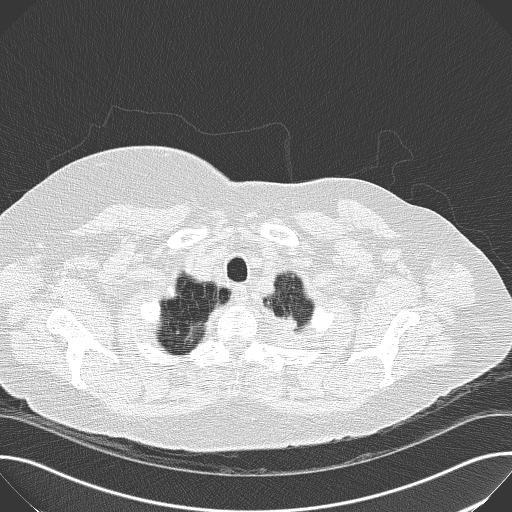
Low-dose screening chest CT, one axial slice; position 155 of 169 along the scan axis; reconstruction kernel B50f; 120 kVp; lung window (W 1500 / L -600 HU); 2 mm slice thickness; 512 × 512 image matrix.
Outlined on this slice (outlined manually by an expert reader):
- lesion 1 (tumor, upper lobe of left lung): box from (x=284, y=316) to (x=298, y=329) px